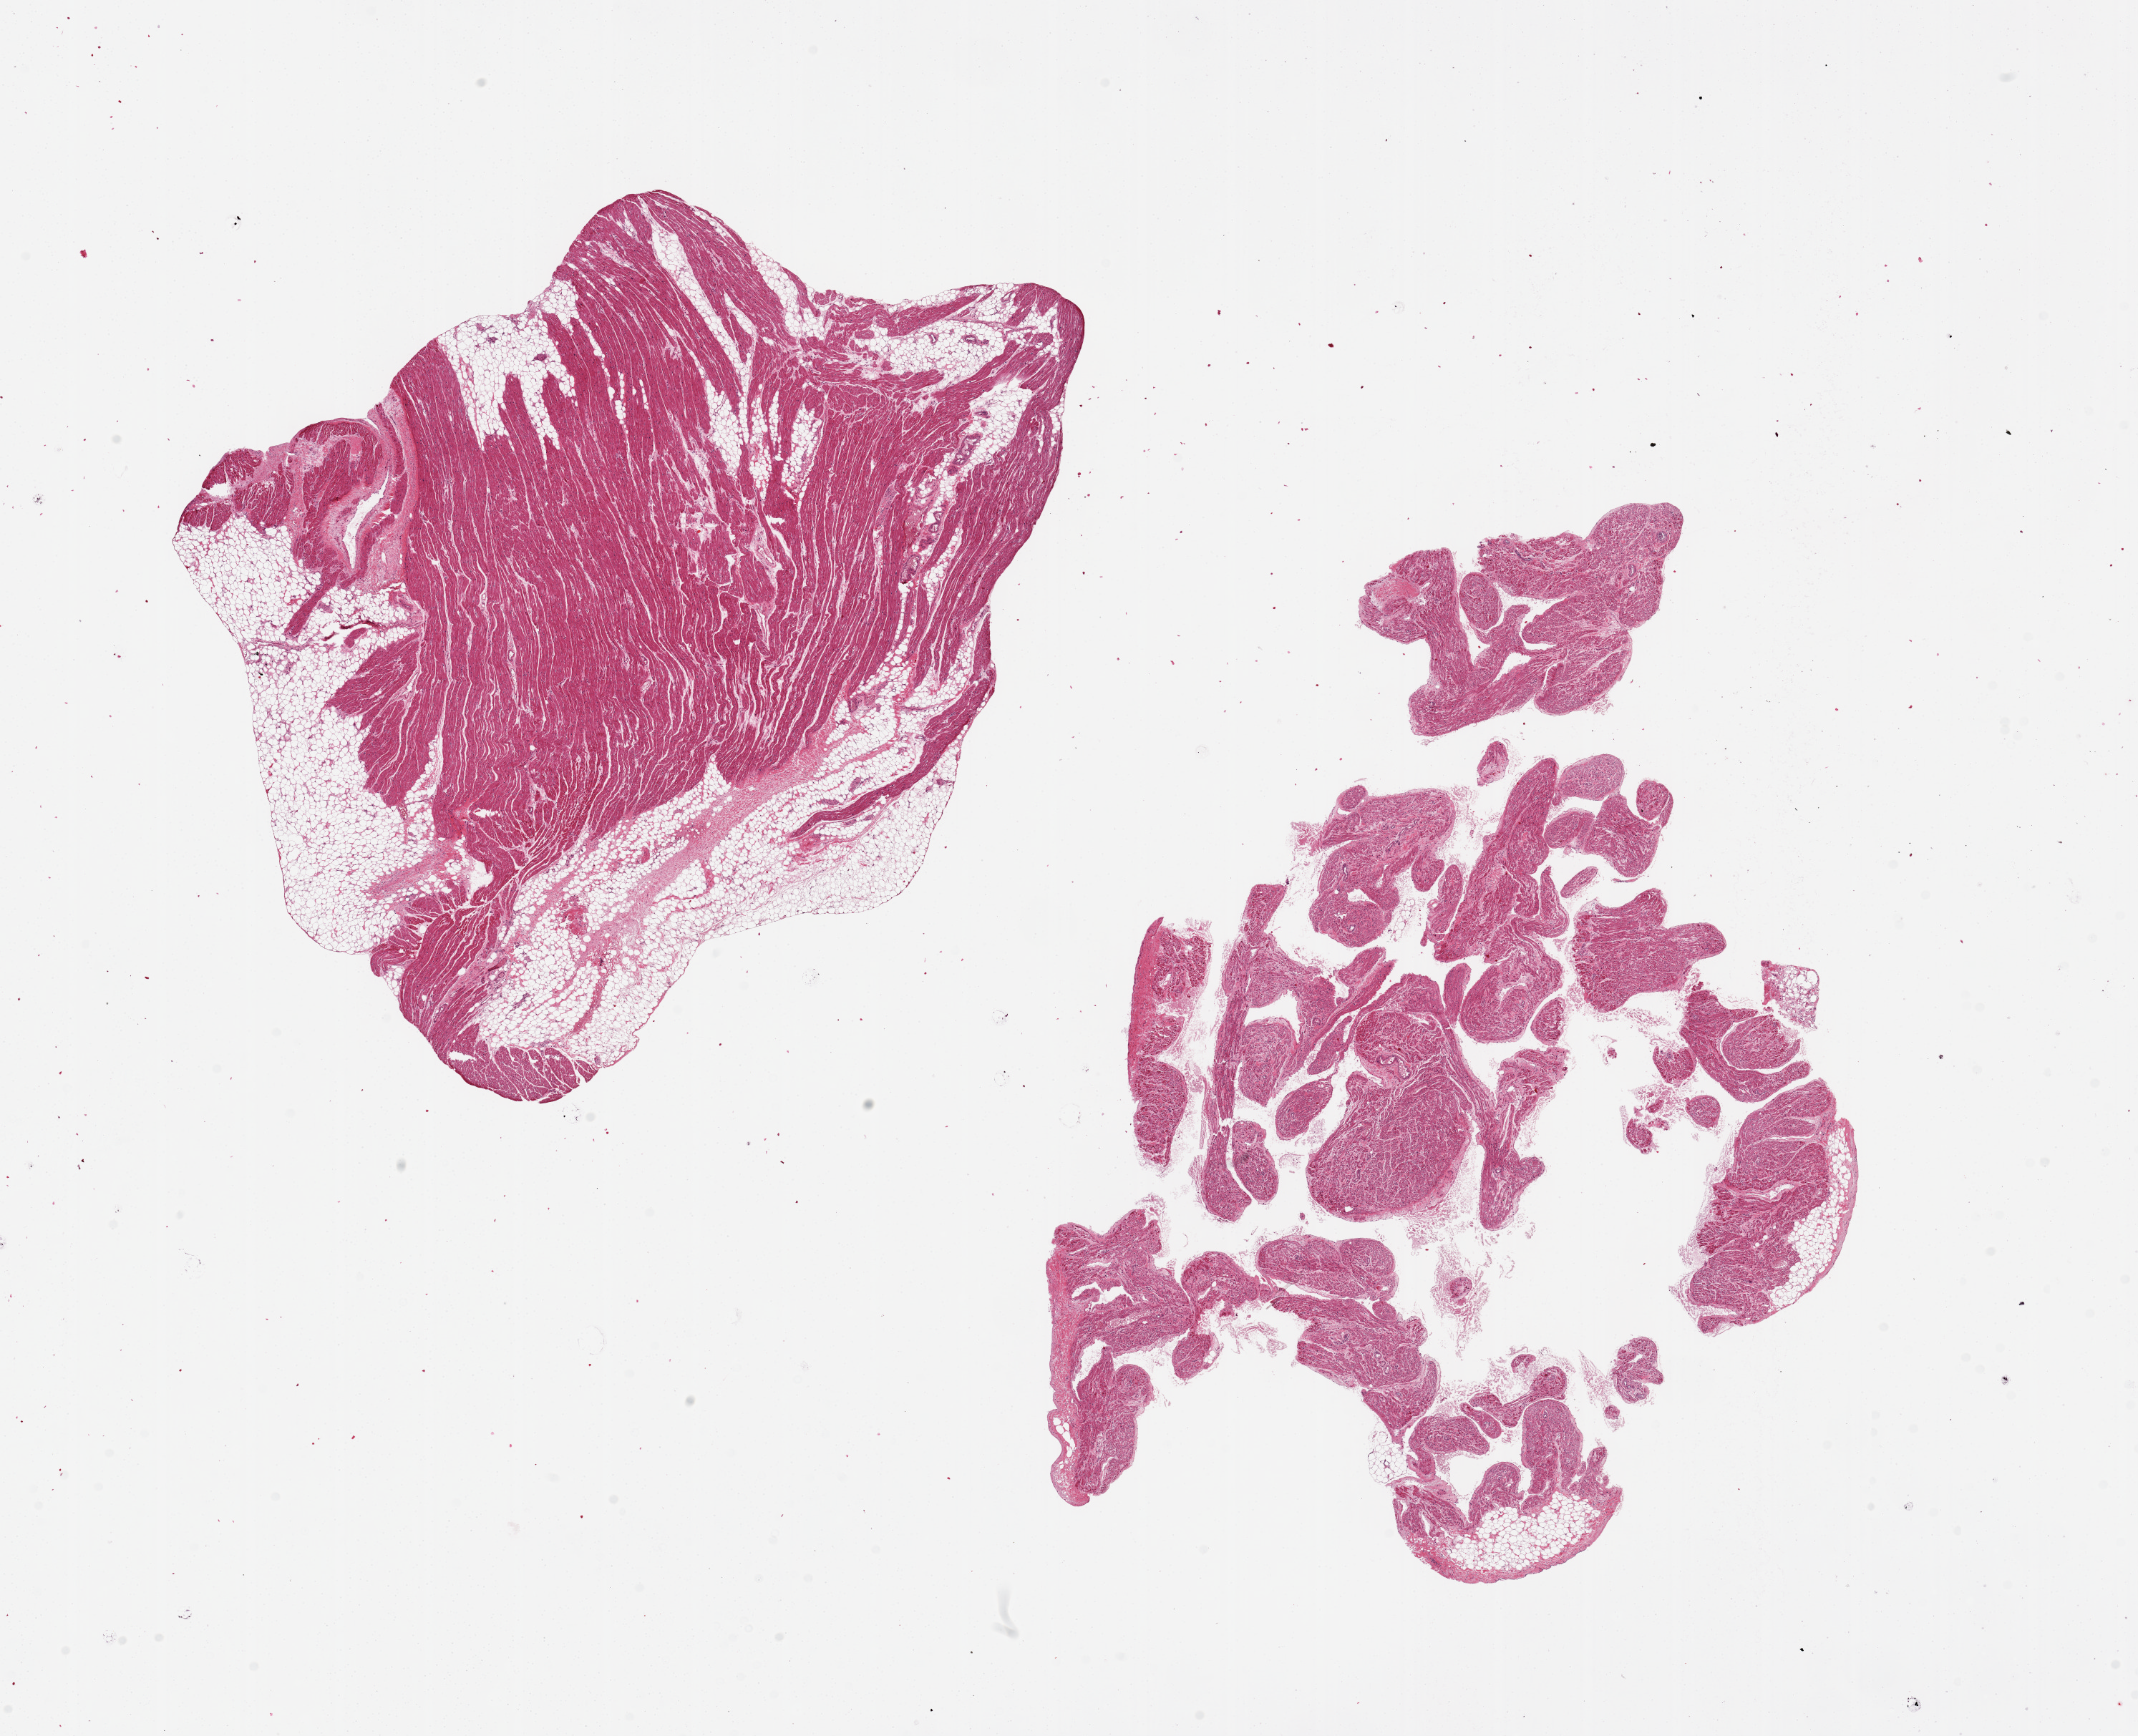
Digitized haematoxylin and eosin-stained section, brightfield — whole scanned area (about 23.6 x 19.2 mm, slide scanned at 20x) shown as a low-resolution overview; PAXgene-fixed, paraffin-embedded tissue; sampled site (target tissue): auricular appendage; tissue donor sample. Donor sex: male.
- review note (as recorded): 2 pieces, 10.5x8 and 13x8mm; 1 with 30% internal fat